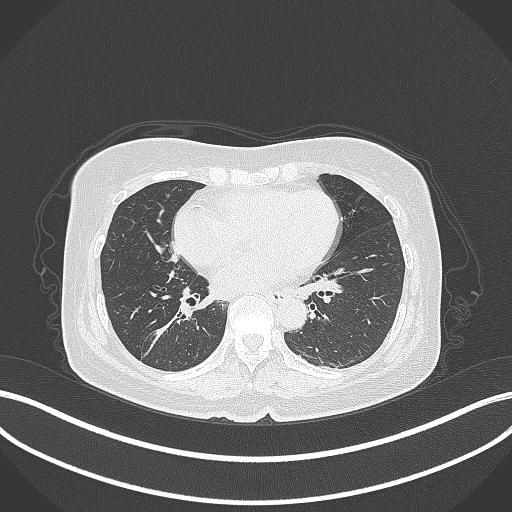
Chest CT, one axial slice; reconstruction kernel B70f; 120 kVp; lung window (W 1500 / L -600 HU); 1 mm slice thickness; 512 × 512 image matrix. Patient: female, 67 years. Case-level facts recorded for this patient, not image findings: clinical TNM (as recorded): T1c N1 M0; histopathological grade: G2-3.
Structures marked on this image (rectangle marked by the reading radiologist):
- lung tumour (recorded histology: adenocarcinoma): box from (x=142, y=307) to (x=192, y=357) px